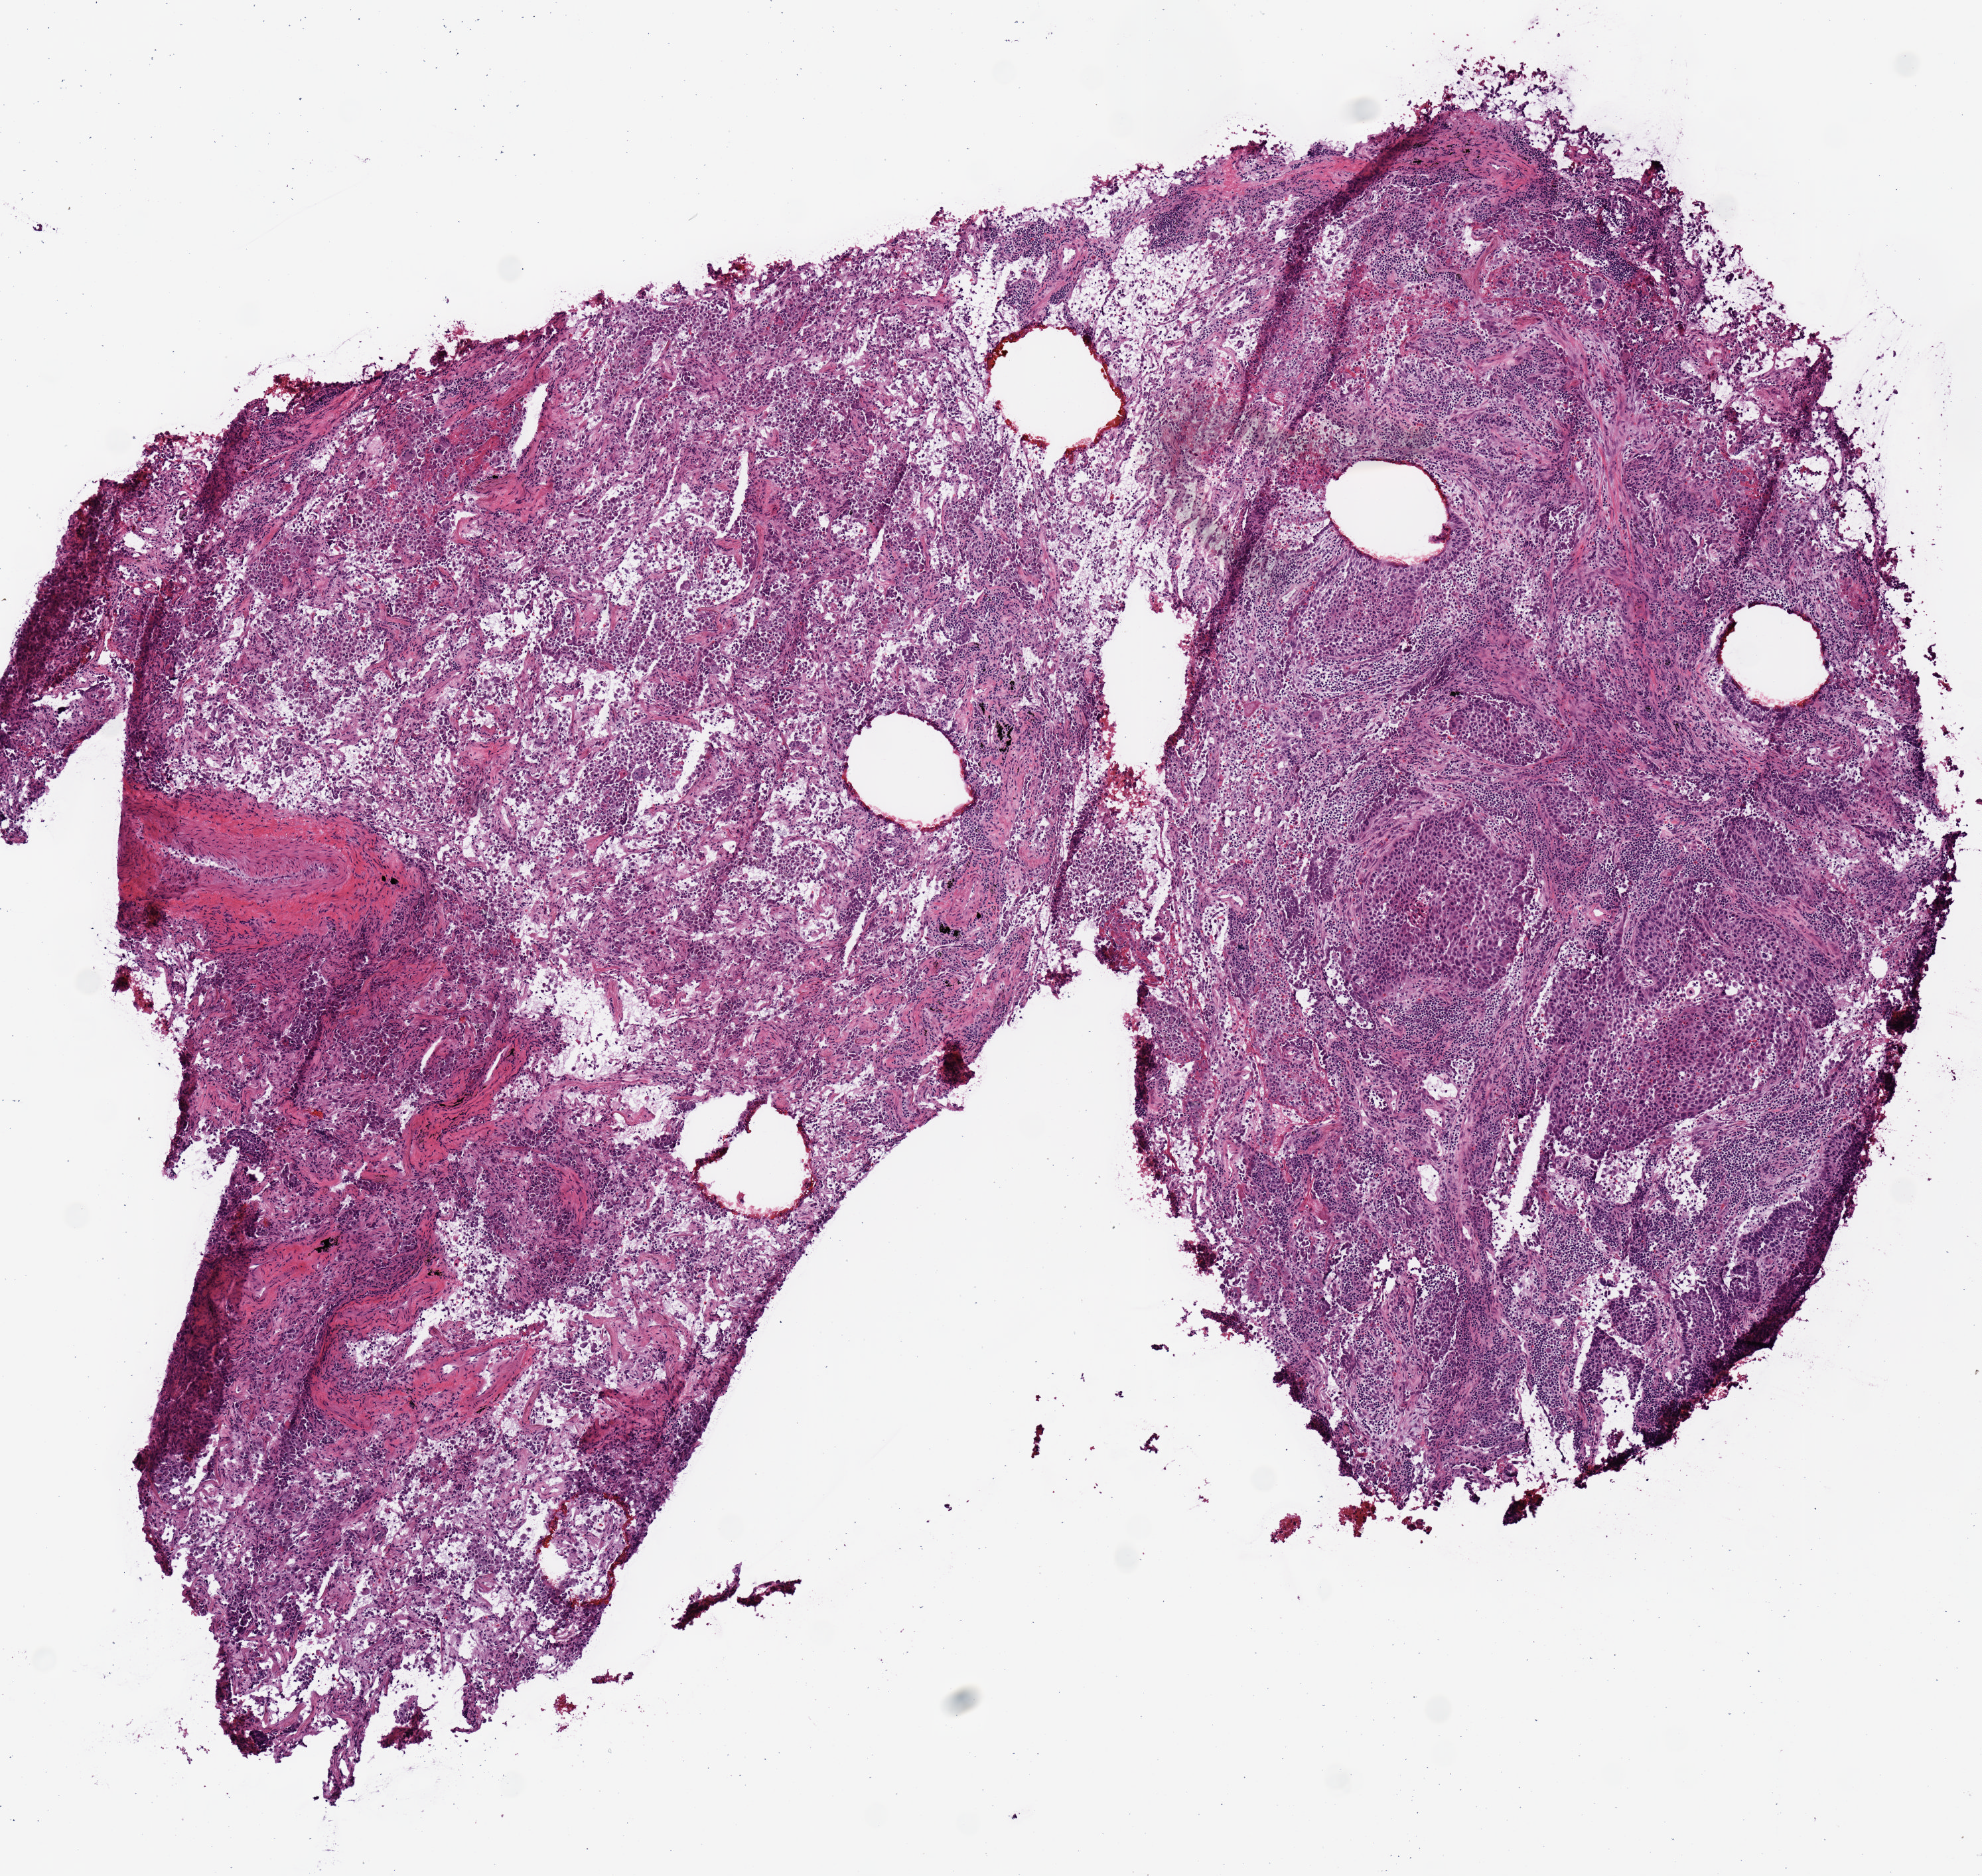
Digitized H&E tissue section (whole slide), shown as a low-resolution overview of the whole scanned area (about 5.9 x 5.6 mm, acquisition: 20x scan). Frozen section. Primary tumour sample from the lung. Male patient; age at initial diagnosis 64 years. Pathologist review of this section (percent, as recorded): tumour nuclei 65%, necrosis 0%.
Laterality: right. Pathologic diagnosis: Squamous cell carcinoma, NOS. AJCC pathologic stage: IIIA (6th edition). TNM: T3 N1 M0.